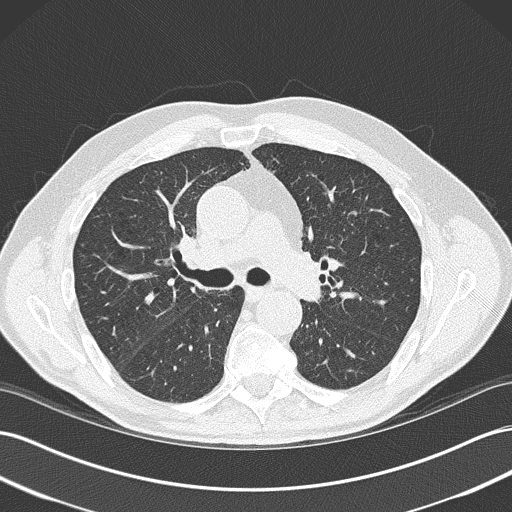
Low-dose screening chest CT, axial slice, baseline screening round, lung window (W 1500 / L -600 HU), lung (sharp) reconstruction kernel (B50f), 120 kVp, slice 100 of 171 in the series. Male, age 73 years at enrolment.
Expert reader's lesion annotation, bounding box <333,199,376,231> (left, top, right, bottom; pixels). The screening reader recorded 2 non-calcified nodules or masses ≥4 mm on this exam (right lower lobe, left upper lobe); which of them this box marks is not recorded. Official screen result: positive, change unspecified: nodule(s) >= 4 mm or enlarging nodule(s), mass(es), or other non-specific abnormalities suspicious for lung cancer. Later outcome: lung cancer diagnosed 400 days after this screen (after the second annual screen) — small cell carcinoma, NOS, left upper lobe, stage IIIB (AJCC 6th edition), 19 mm at pathology.